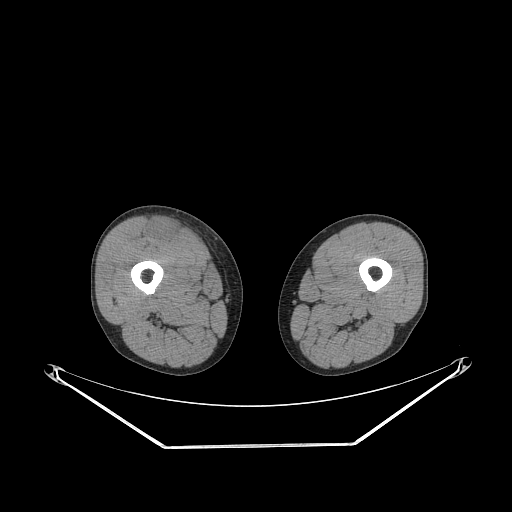
CT of an extremity soft-tissue mass (from a PET/CT study), one axial slice. Slice 243 of 311 in the series (ordered by position). Reconstruction kernel STANDARD. Soft-tissue window (W 400 / L 40 HU). 512 × 512 image matrix. Male patient. From the clinical record (not read from this slice): histological type: pleiomorphic leiomyosarcoma; grade: intermediate; site of the primary tumour: right thigh.
Structures marked on this image (expert contour drawn on MRI and transferred to this co-registered scan by the dataset authors):
- gross tumour volume including surrounding oedema: bounding box <149,219,182,243> (left, top, right, bottom; pixels)